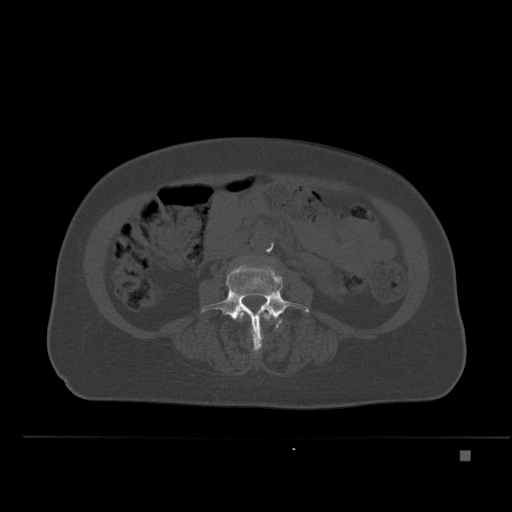
CT including the spine, one axial slice; bone window (W 1800 / L 400 HU); 512 × 512 image matrix, field of view 422 × 422 mm. Female patient, age 74 years. From the clinical record (not read from this slice): primary cancer: colon.
Outlined on this slice (semi-automatic segmentation, software-assisted and operator-edited):
- L3 vertebra: box from (x=239, y=310) to (x=271, y=322) px
- L4 vertebra: (x=201, y=265)–(x=309, y=350)